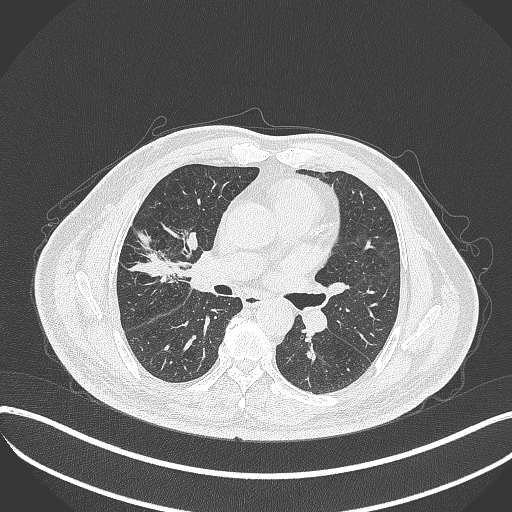
Chest CT, one axial slice. Position 199 of 401 along the scan axis. Lung window (W 1500 / L -600 HU). 1 mm slice thickness. 512 × 512 image matrix. Male patient, age 72 years. Case-level facts recorded for this patient, not image findings: clinical TNM (as recorded): T1c N0 M0.
Structures marked on this image (rectangle marked by the reading radiologist):
- lung tumour (recorded histology: squamous cell carcinoma): bounding box [x1, y1, x2, y2] px = [176, 230, 214, 297]